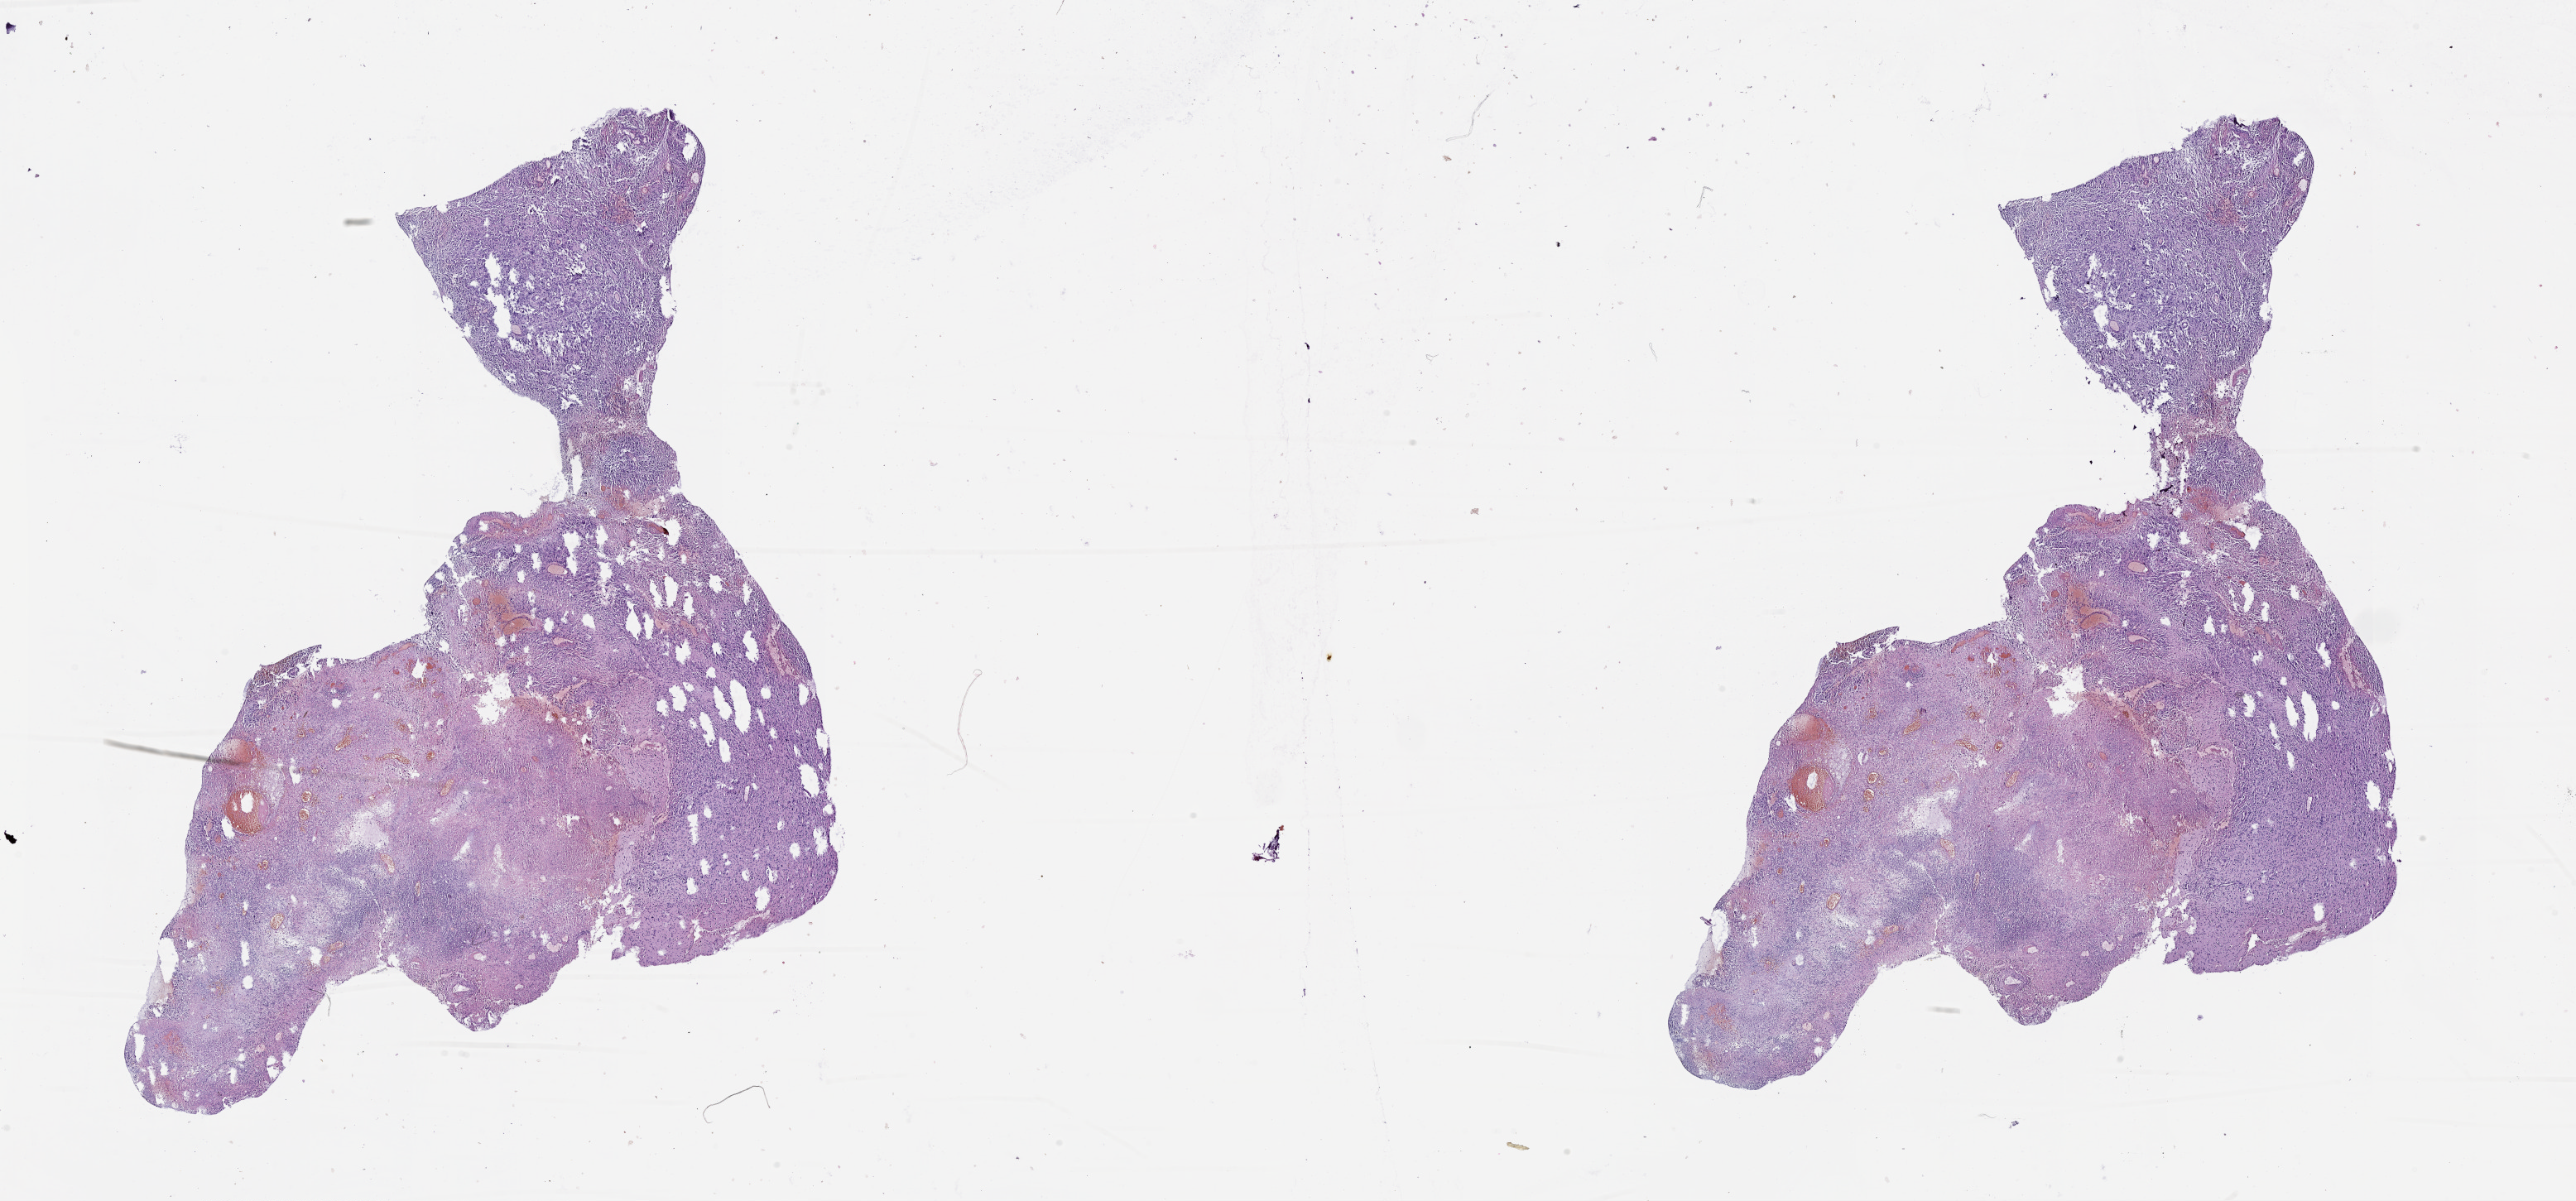
H&E whole-slide image, a low-resolution overview of the entire scanned area, about 25.1 x 11.7 mm (slide scanned at 20x). Brain, tumour tissue. Patient: male, age 63 years.
Histologic diagnosis: Glioblastoma. Primary tumour site (as recorded): frontal lobe.